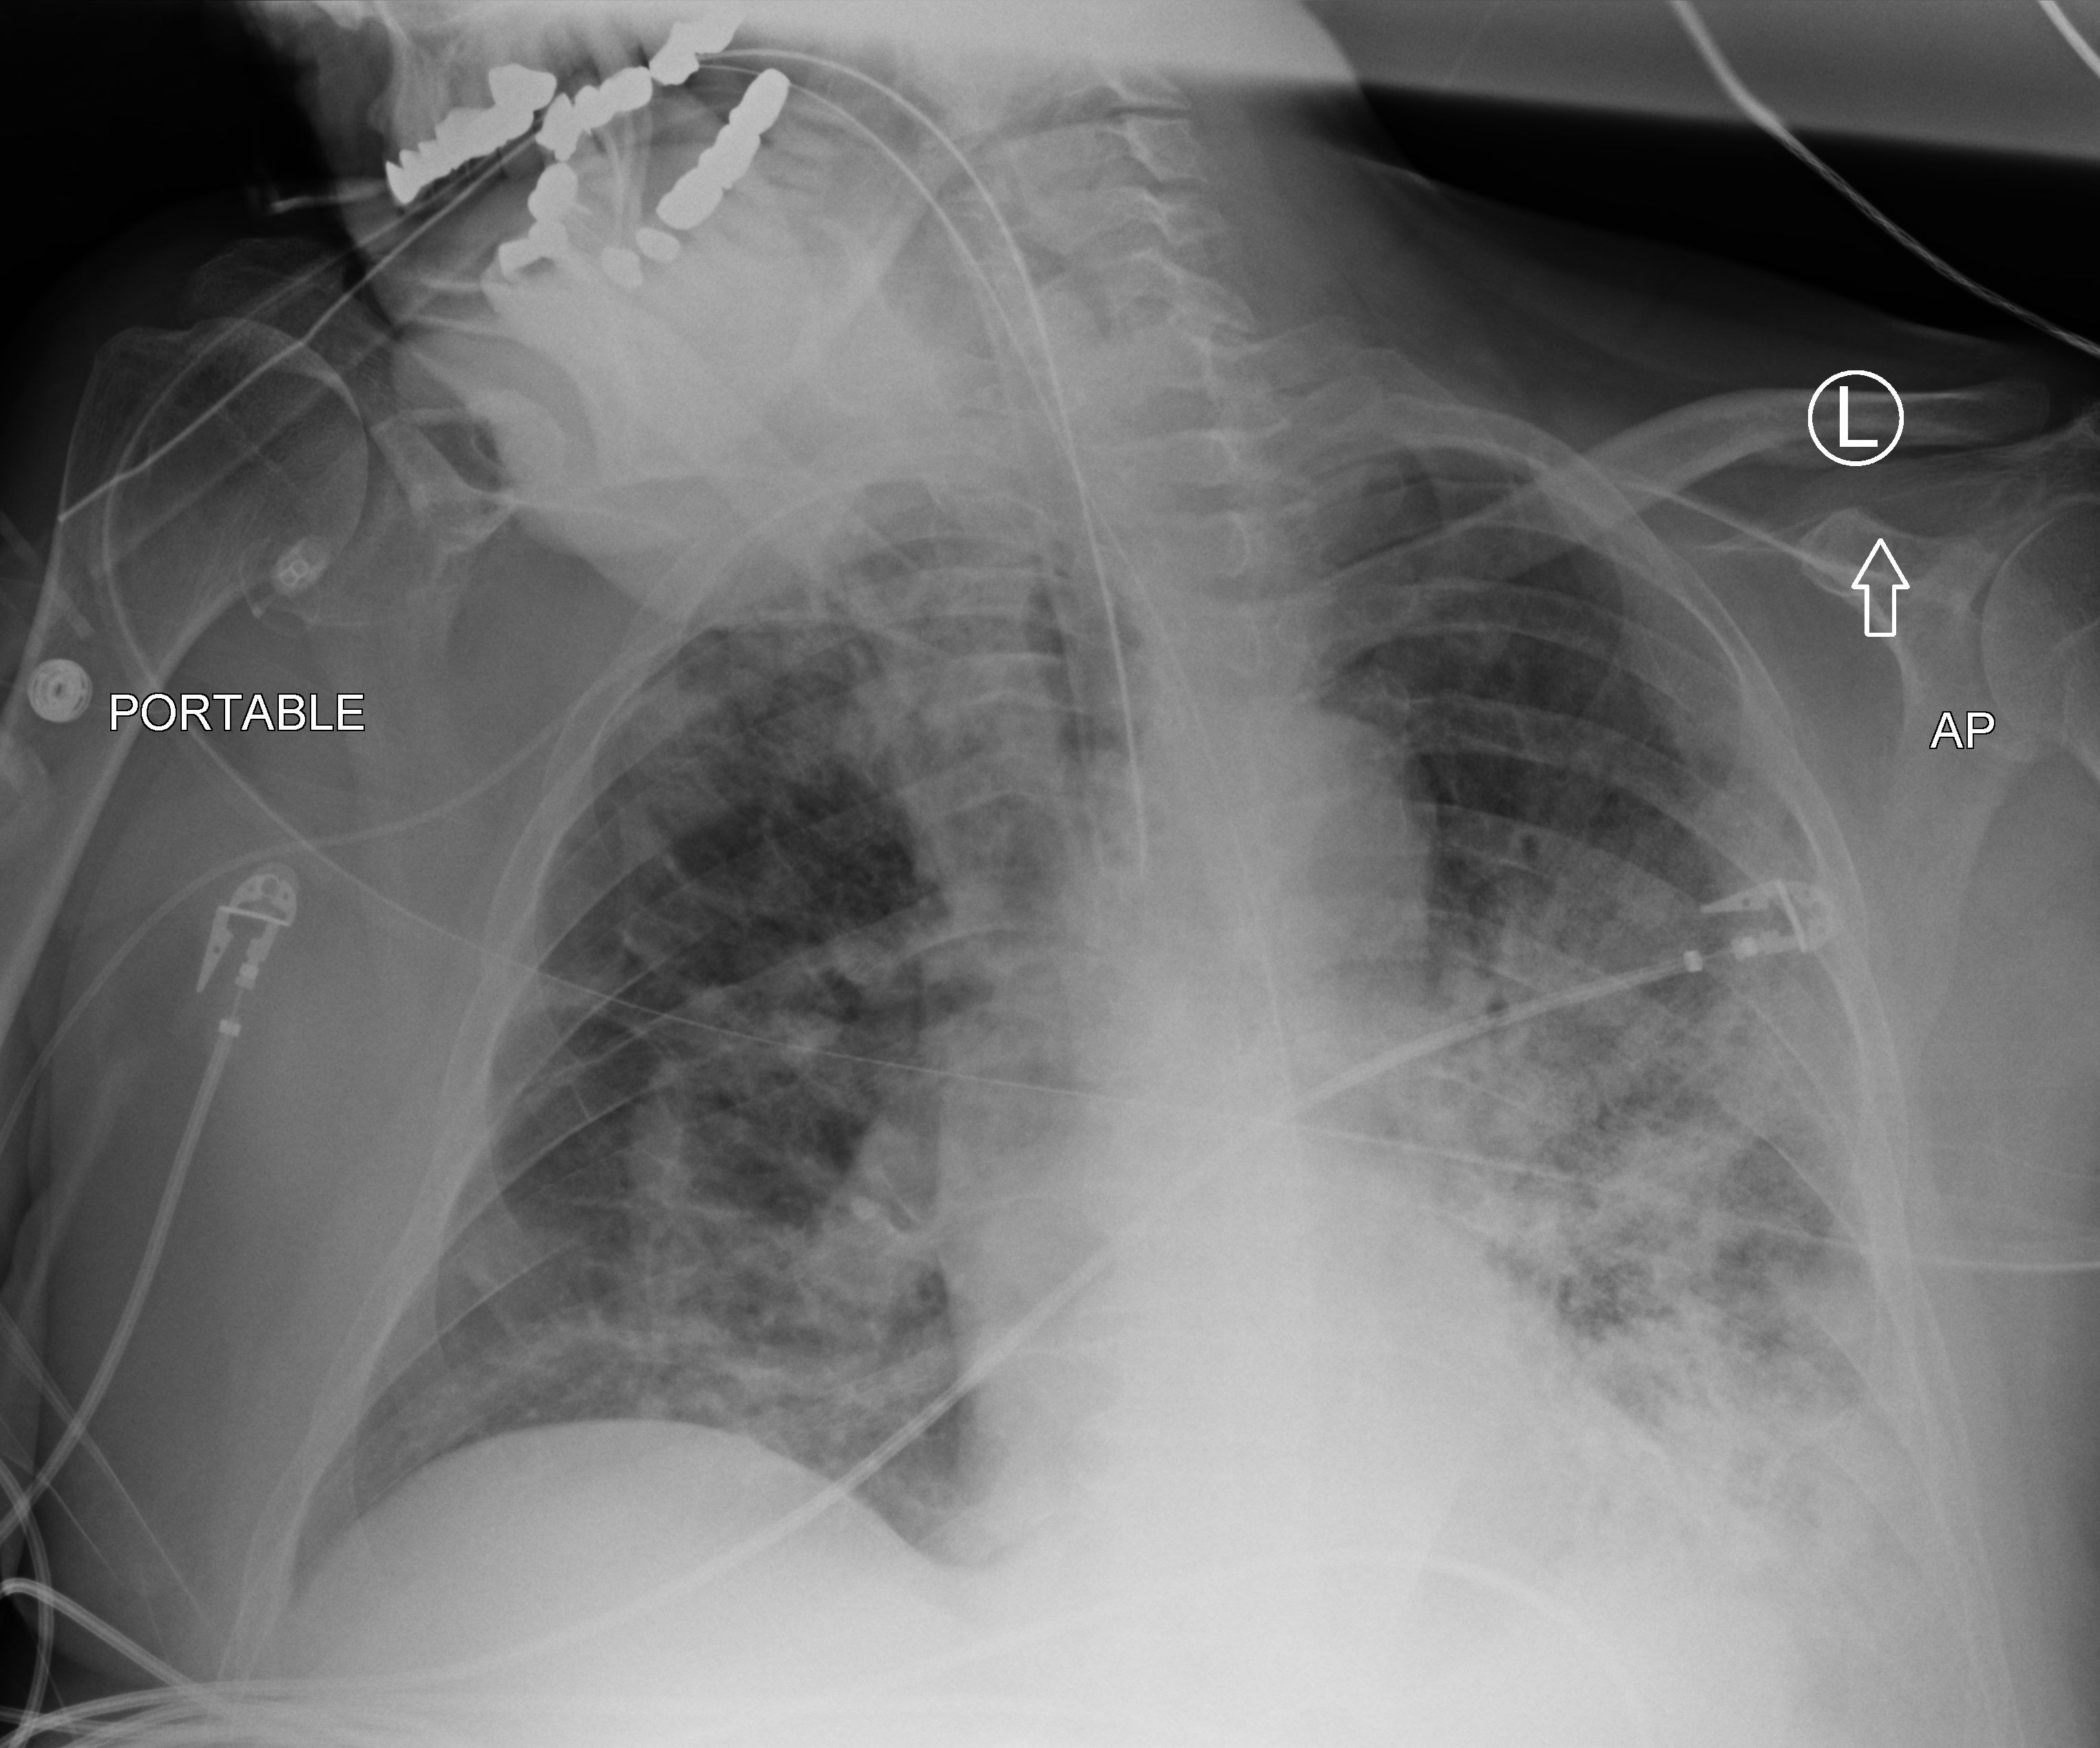
Bedside chest radiograph (computed radiography), anteroposterior (AP) projection. Patient hospitalised with COVID-19; male, aged 60–74 years.
From the hospital-stay record, not from the radiograph (when in the stay this image was taken is not recorded): length of hospital stay: 24 days; mechanically ventilated during this hospital stay: yes.